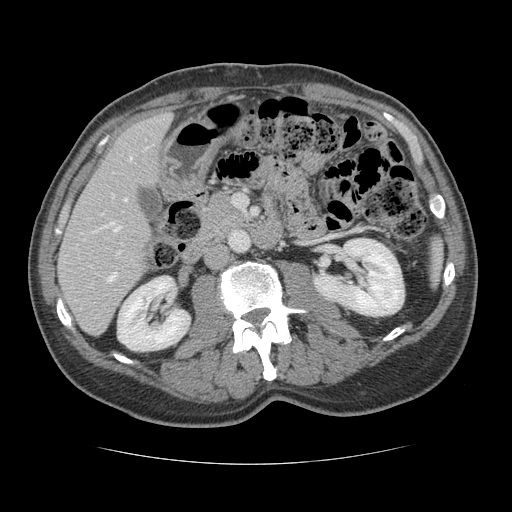
Contrast-enhanced abdominal CT, one axial slice. Slice 56 of 134 in the series (ordered by position). Reconstruction kernel STANDARD. Intravenous contrast given. Soft-tissue window (W 400 / L 40 HU). 2.5 mm slice thickness. 512 × 512 image matrix. Male patient, age 68 years. From the clinical record (not read from this slice): diagnosis: colorectal cancer liver metastases, imaged before liver resection; multiple liver metastases: yes; largest metastasis: 2.2 cm; disease in both lobes: no.
Outlined on this slice (manually delineated by an expert):
- hepatic veins: bounding box <103,157,132,231> (left, top, right, bottom; pixels)
- liver: <59,114,170,334>
- planned liver remnant (the part of the liver to remain after resection): <59,114,170,334>
- portal vein (with intrahepatic branches): <108,251,120,282>